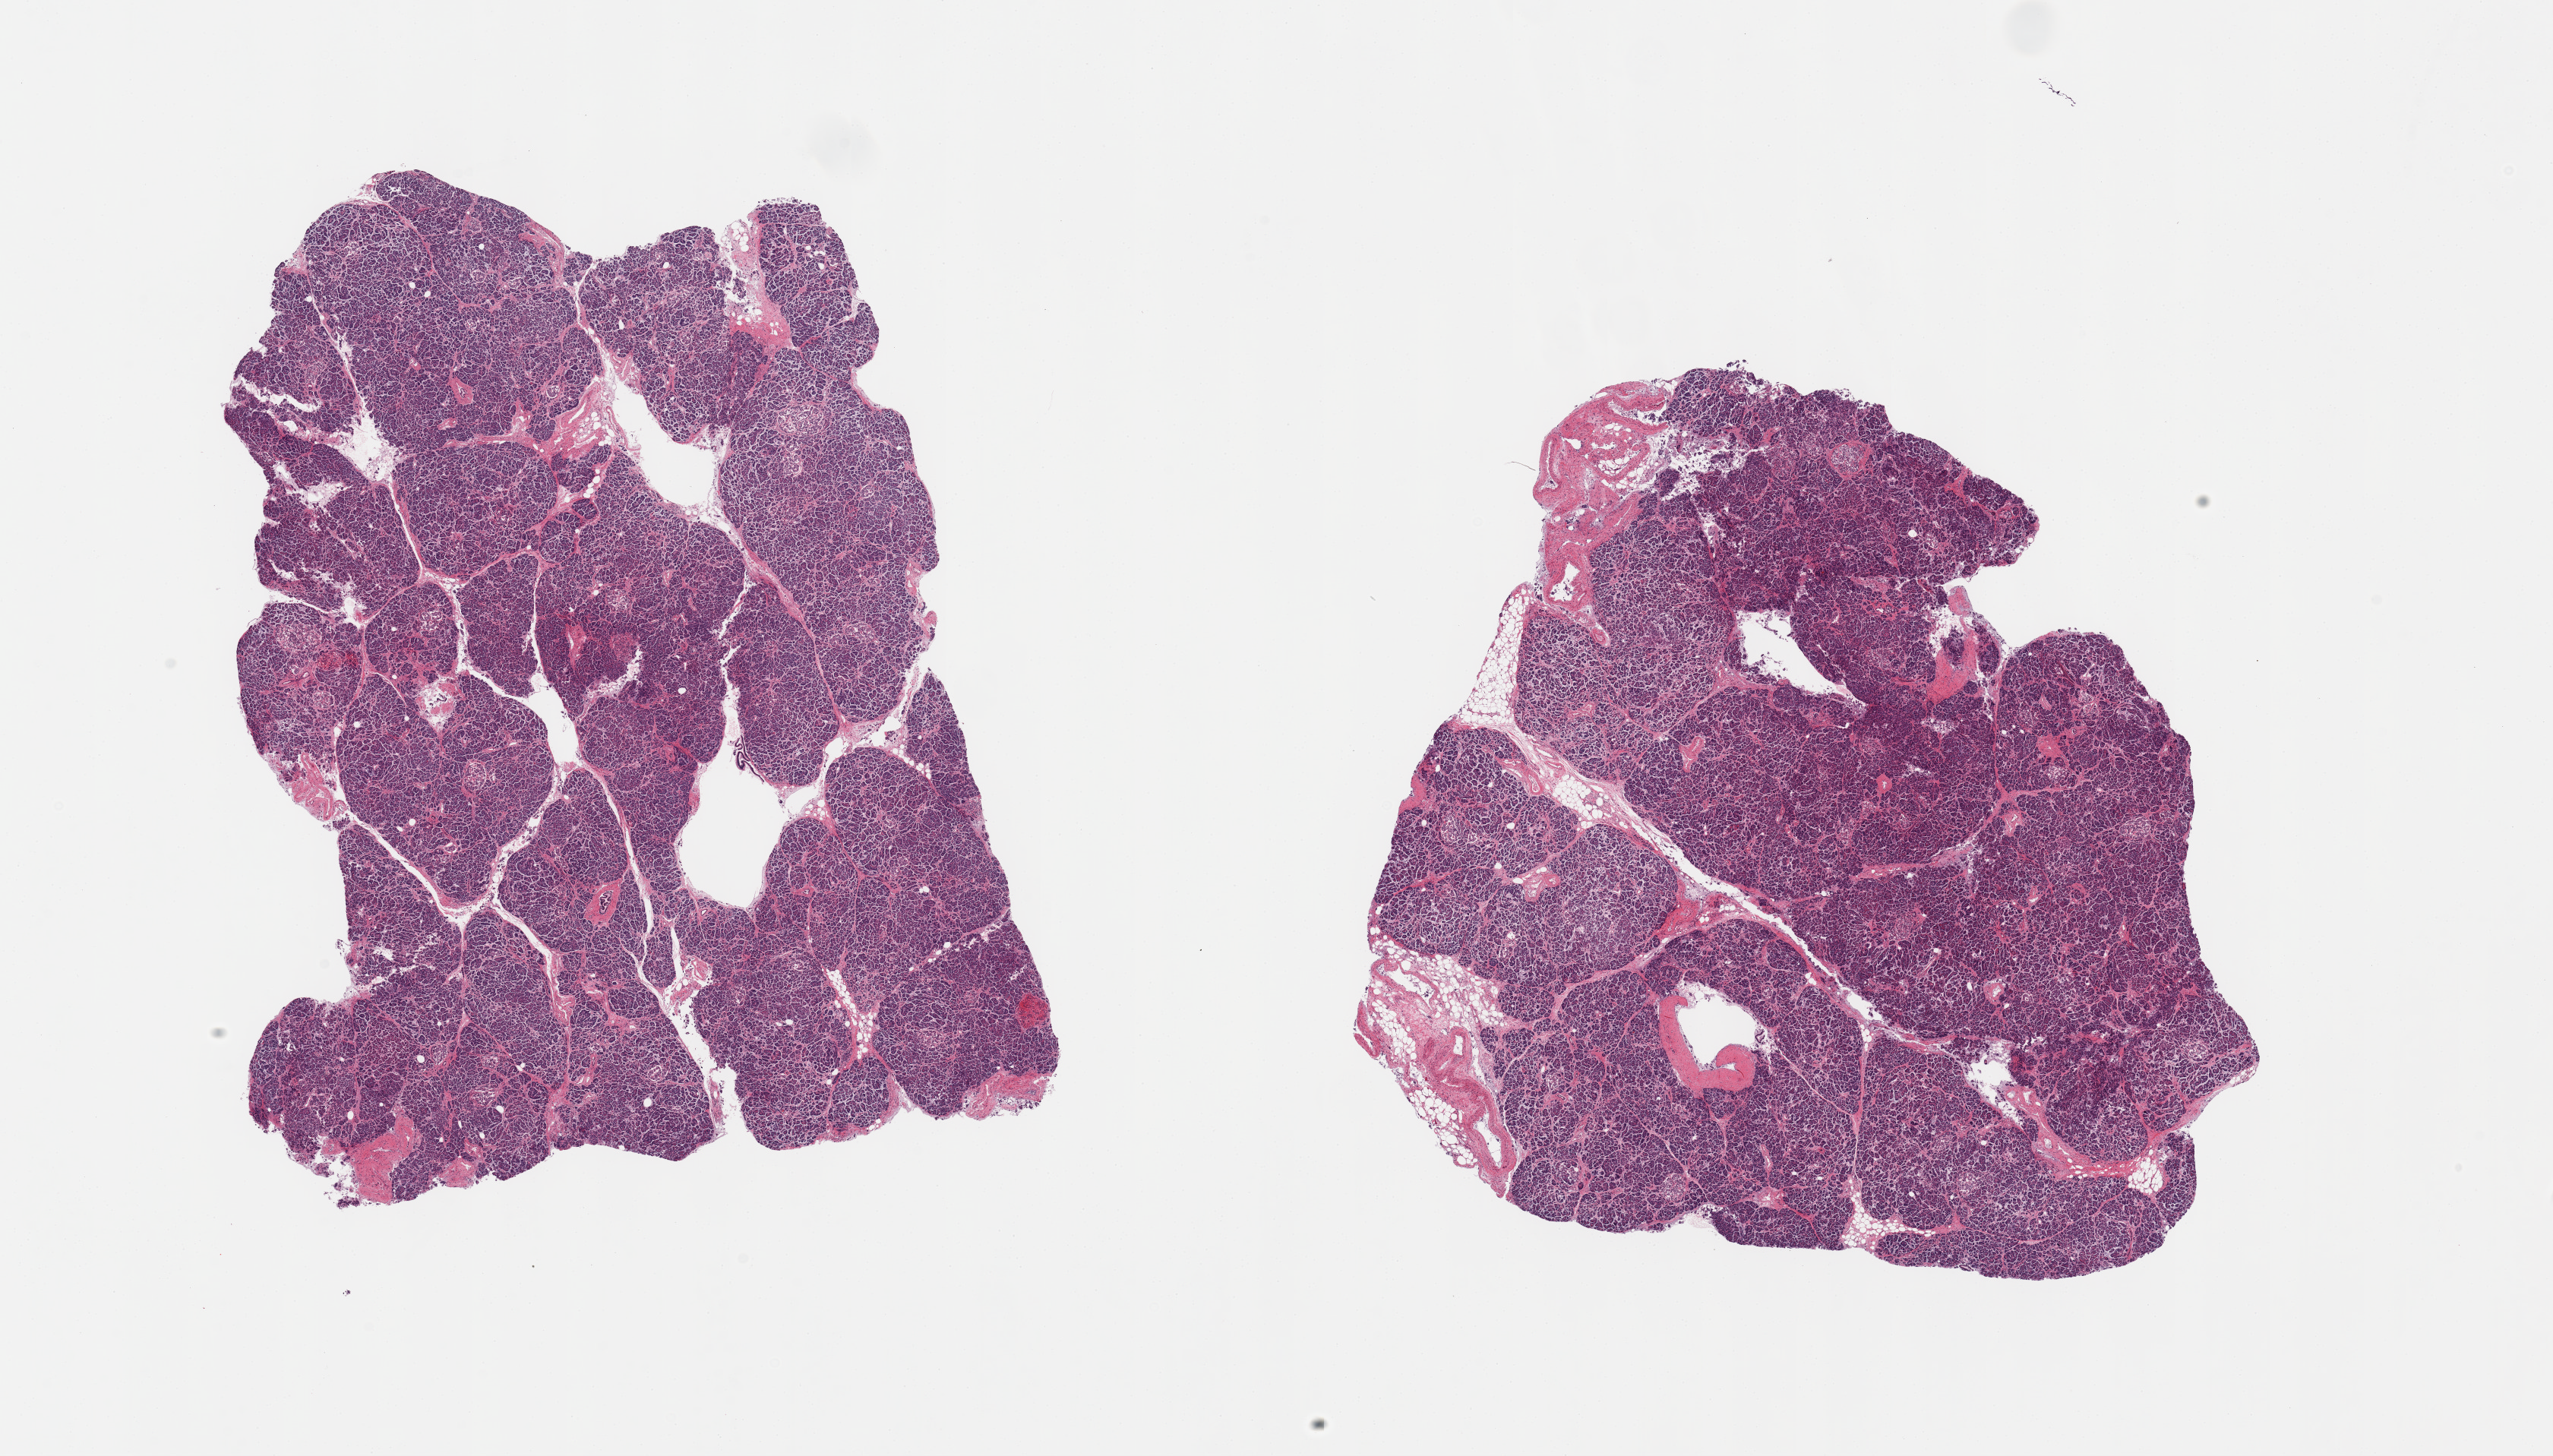
Haematoxylin and eosin whole-slide image, brightfield — shown as a low-resolution overview of the whole scanned area (about 26.6 x 15.2 mm). PAXgene-fixed paraffin-embedded (PFPE) section. Target tissue: pancreas. Donor tissue sample. Male donor.
- reviewer comment on this tissue sample: 2 pieces; no alteration in islet cell content